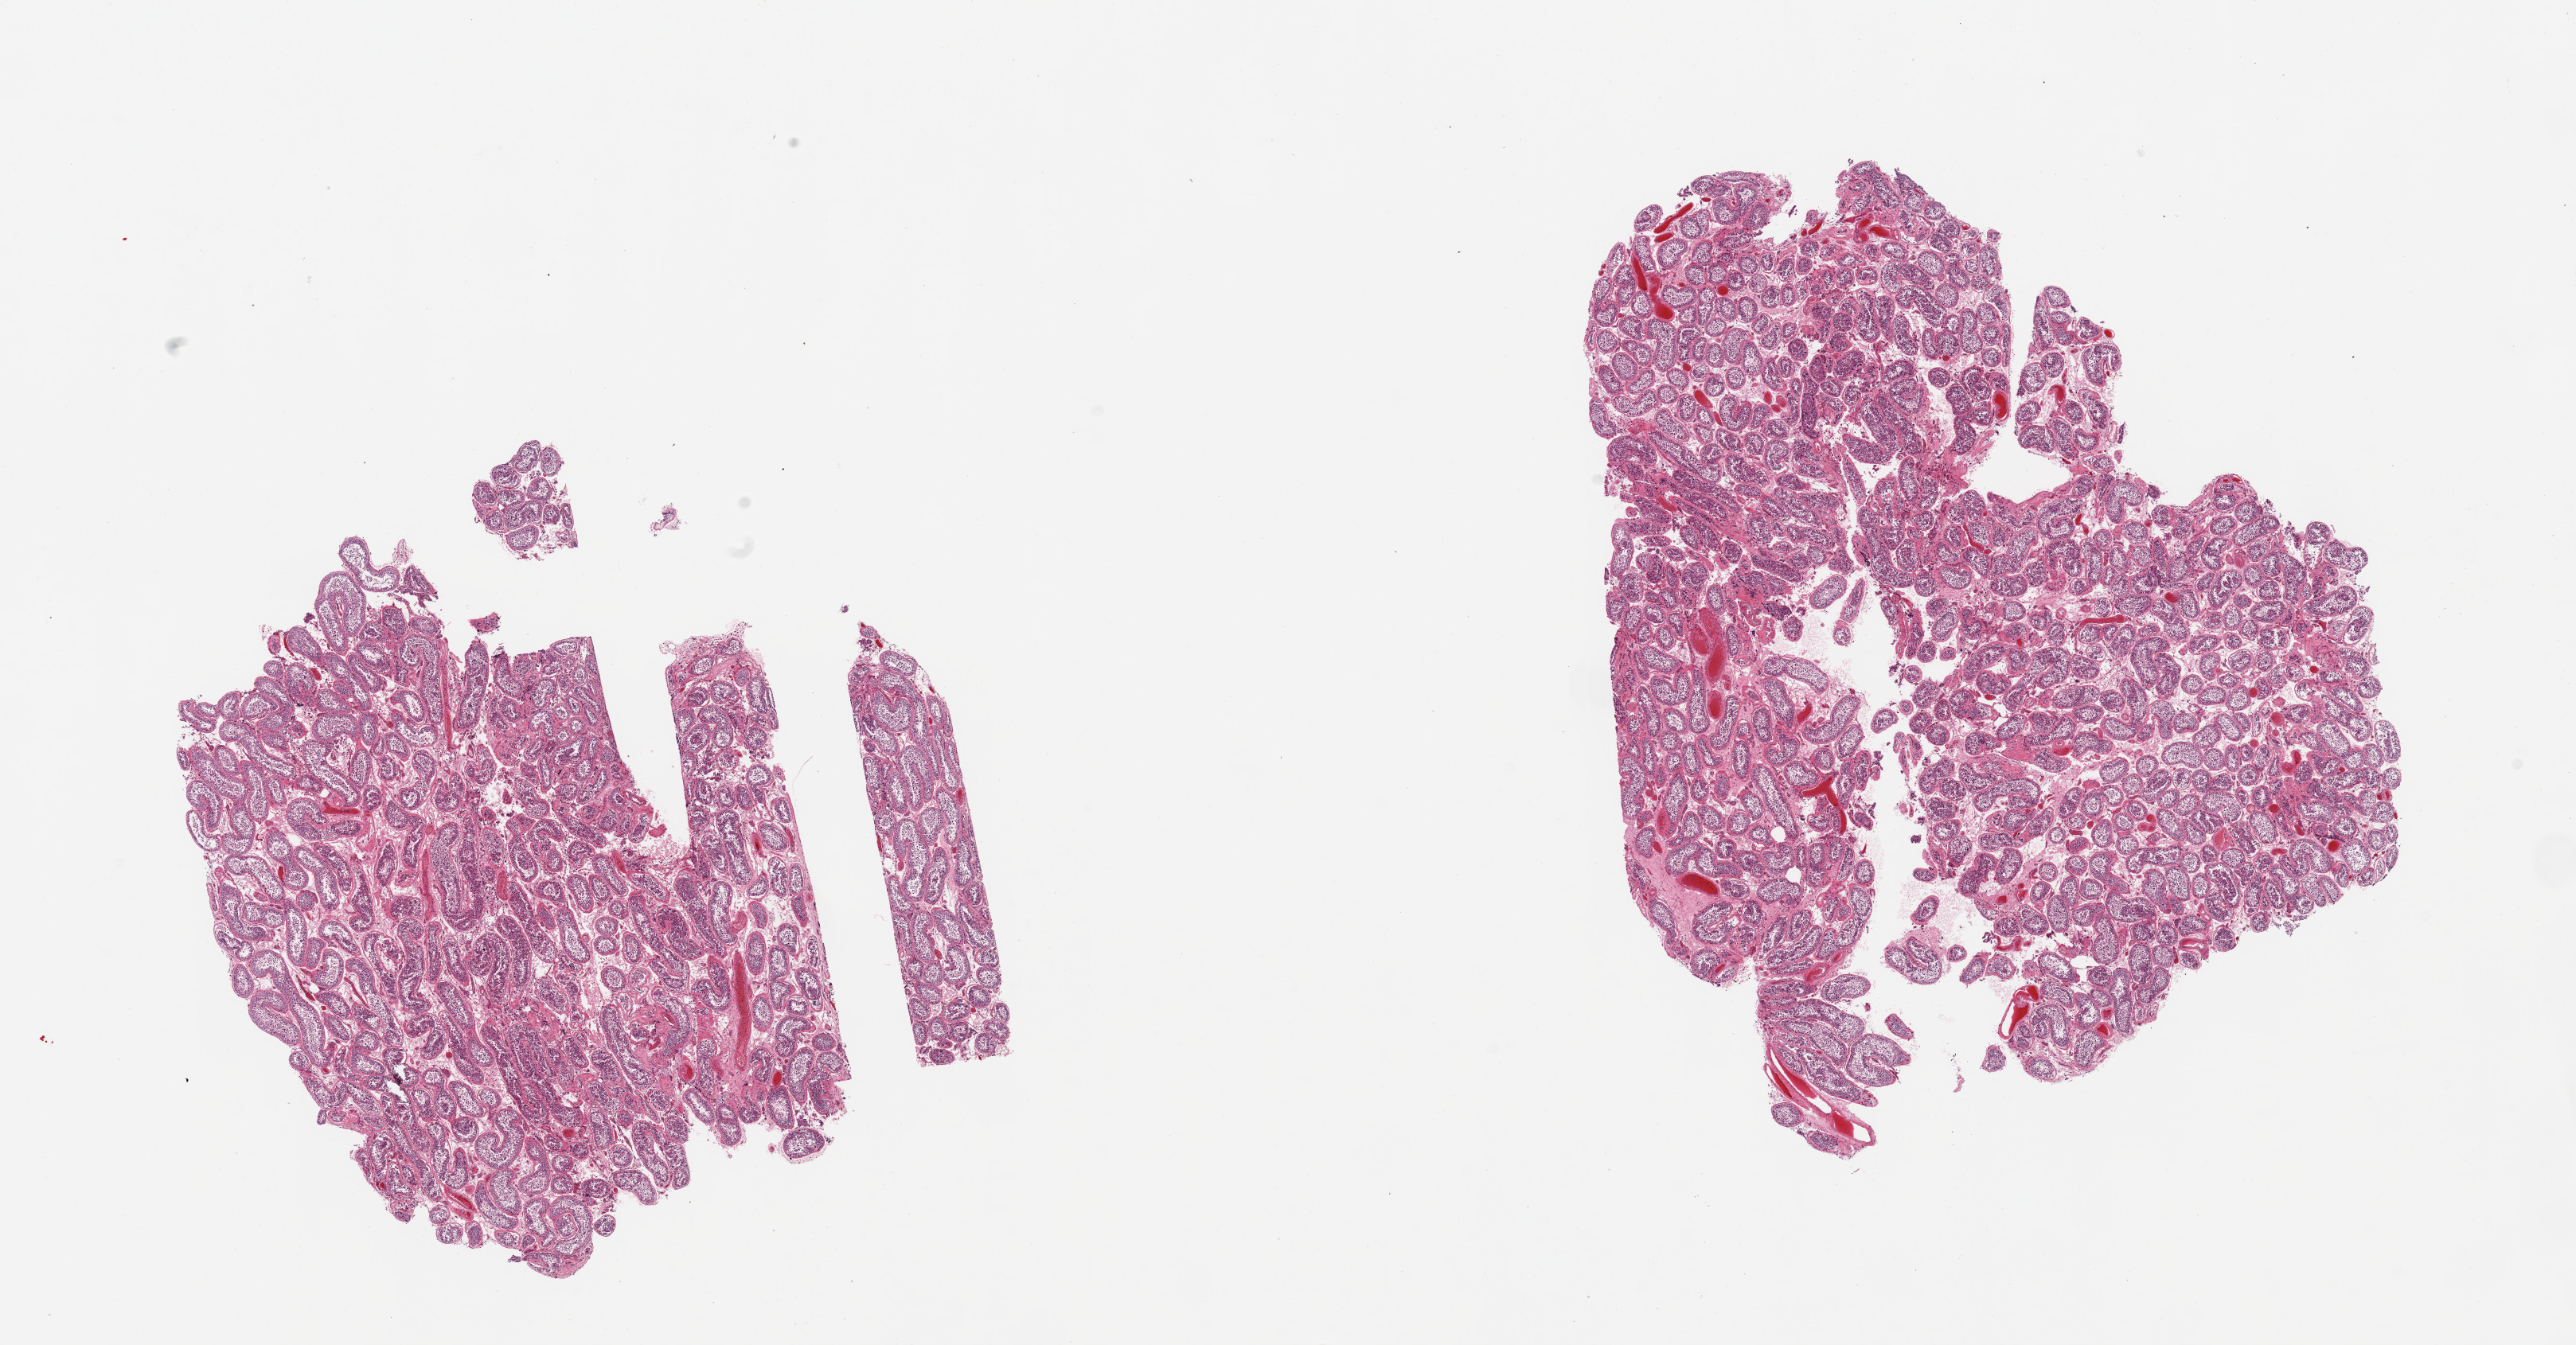
Haematoxylin and eosin whole-slide image, shown as a low-resolution overview of the whole scanned area (about 25.6 x 13.4 mm), PAXgene-fixed, paraffin-embedded tissue, target tissue: testis, donor tissue sample. Male donor.
Pathologist's review note for this sample: 2 pieces, moderately autolyzed, evidence of spermatogenesis.